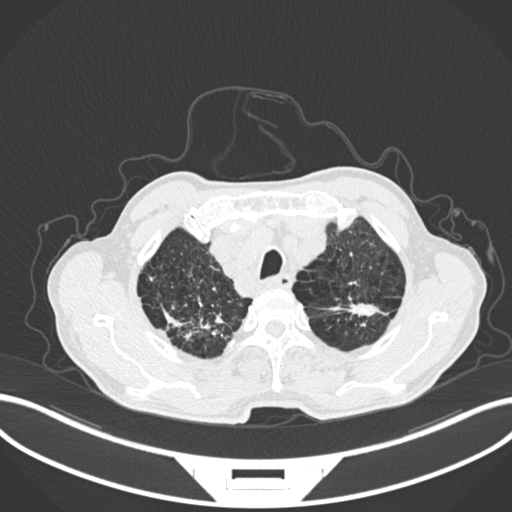
Chest CT, one axial slice; position 238 of 287 along the scan axis; lung window (W 1500 / L -600 HU); 512 × 512 image matrix, field of view 400 × 400 mm. Male patient, age 74 years. From the clinical record (not read from this slice): clinical TNM (as recorded): T2a N1 M0.
Annotated regions visible in this slice (rectangle marked by the reading radiologist):
- lung tumour (recorded histology: adenocarcinoma): bounding box [x1, y1, x2, y2] px = [336, 296, 383, 320]